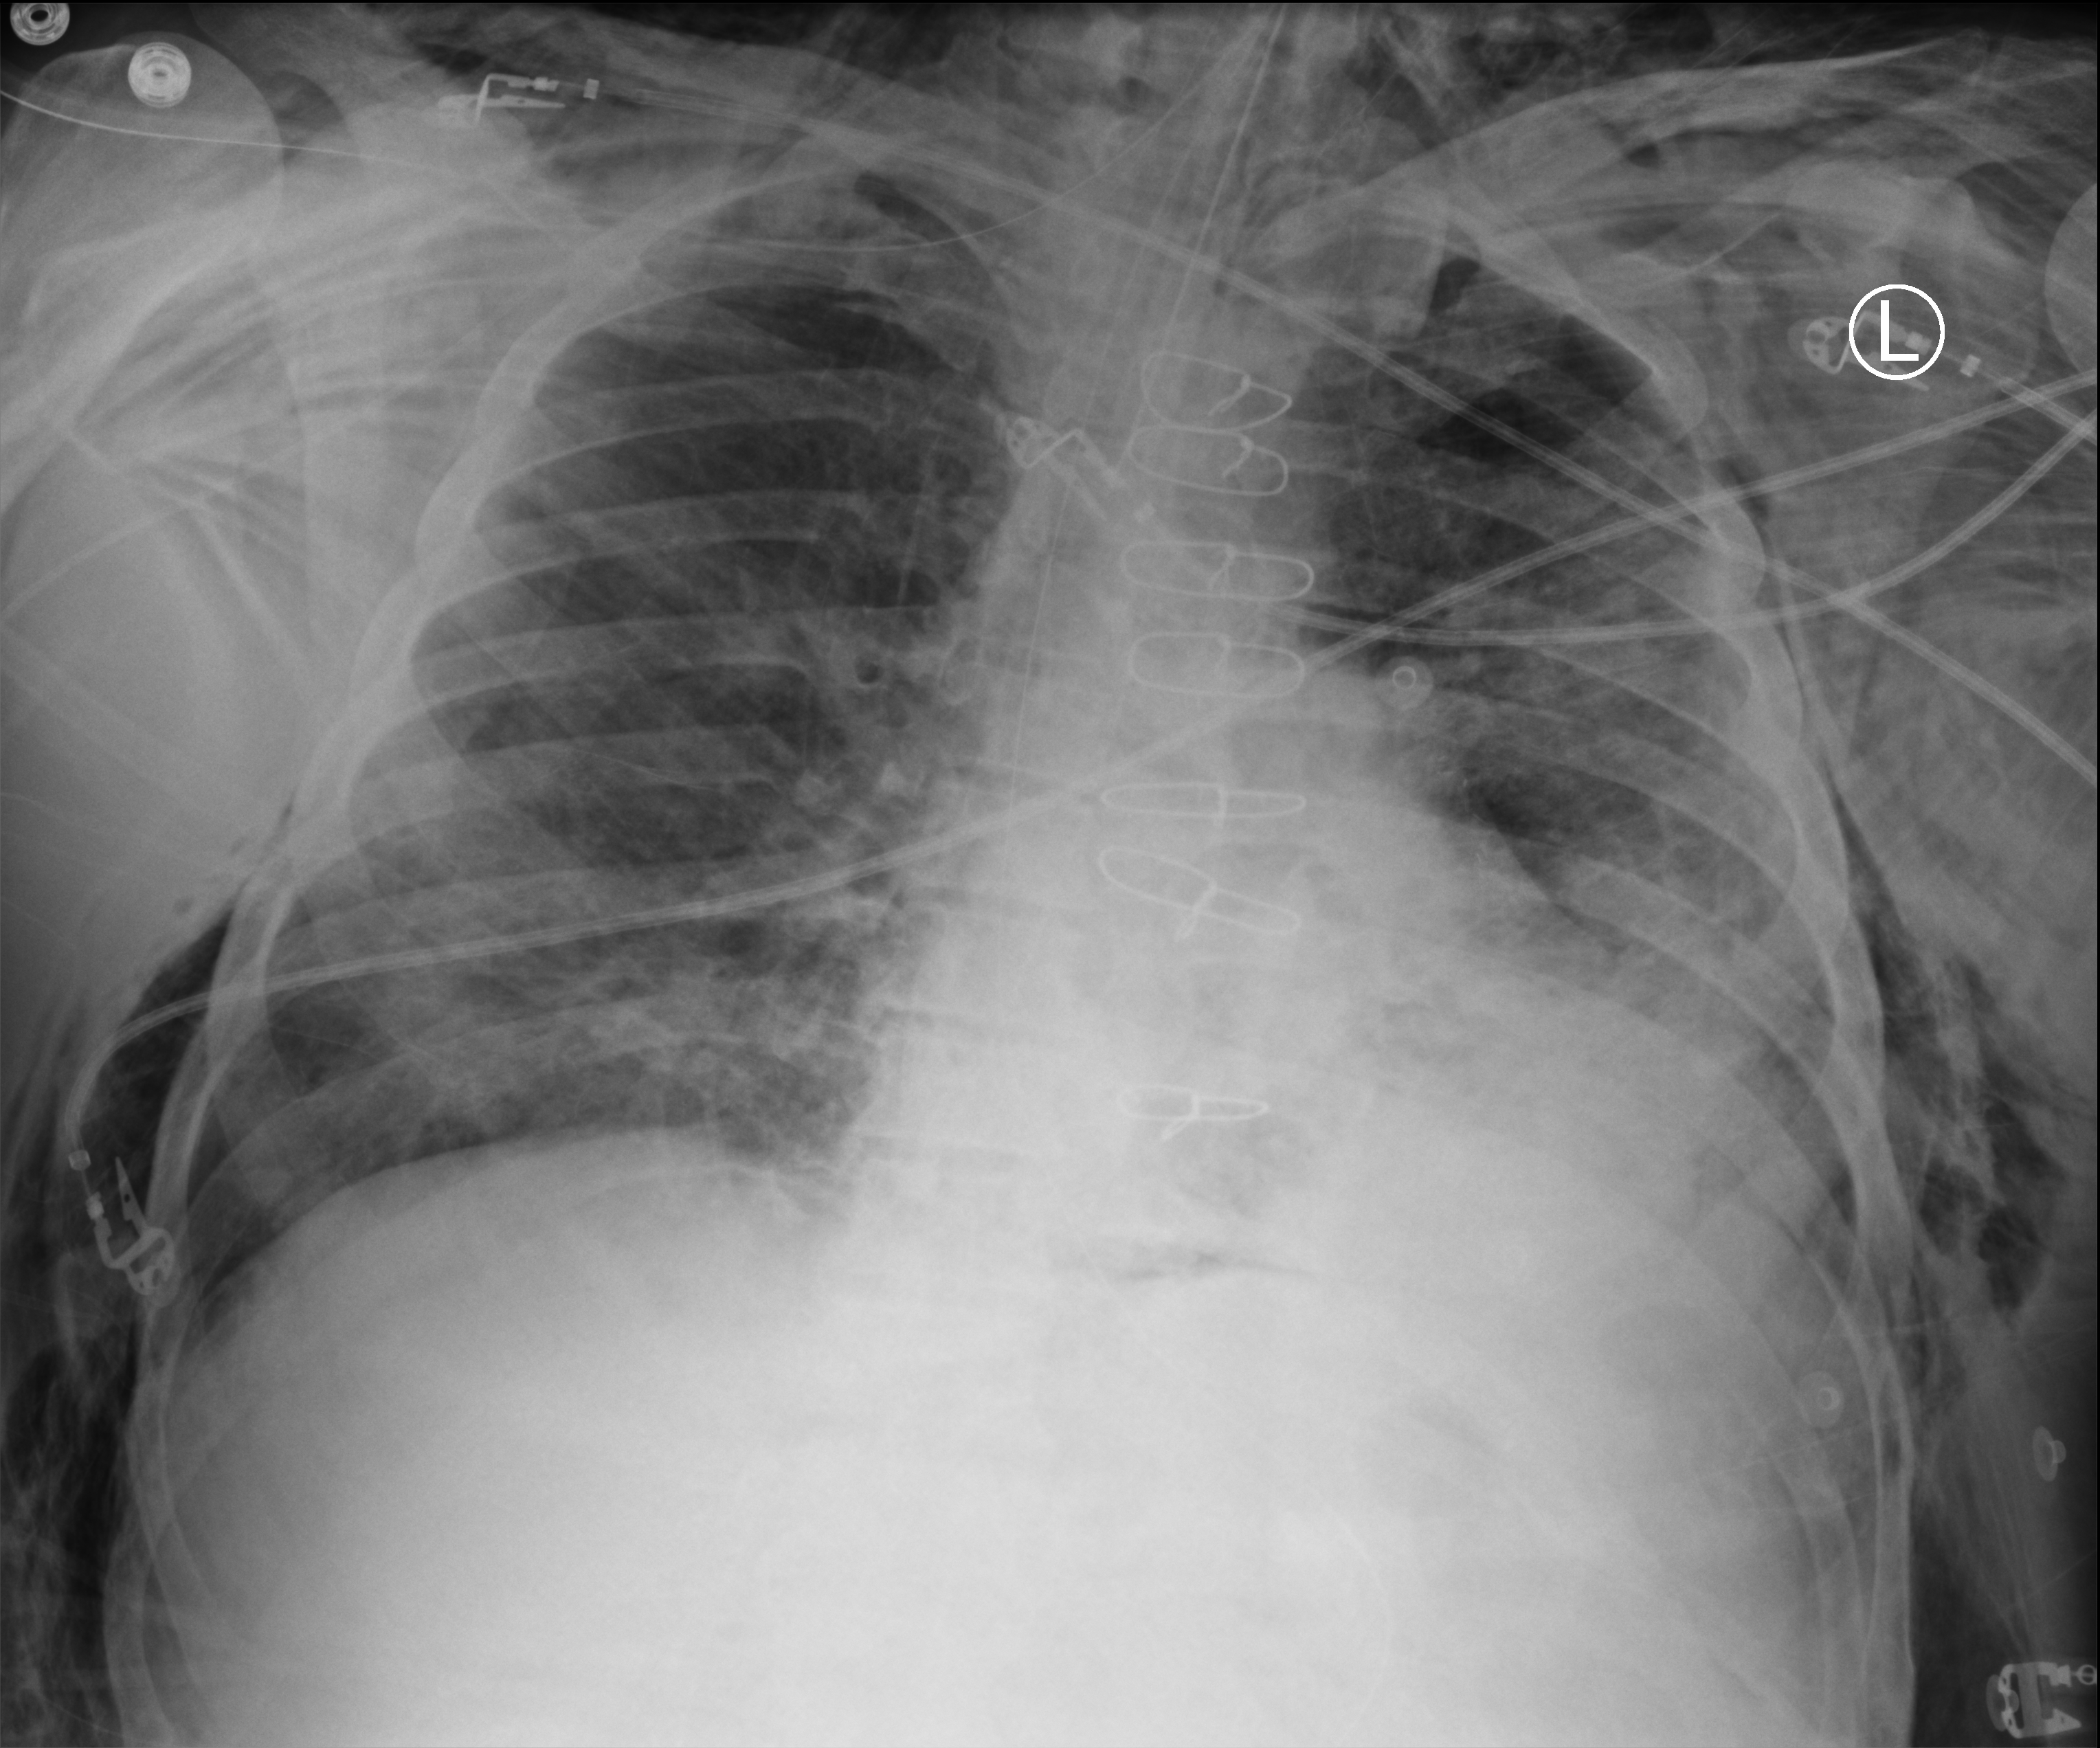
Chest X-ray (portable). Male patient hospitalised with COVID-19, age 60–74 years.
Admission-level facts for this patient (not findings on this image; timing relative to this image not recorded): length of hospital stay: 44 days.